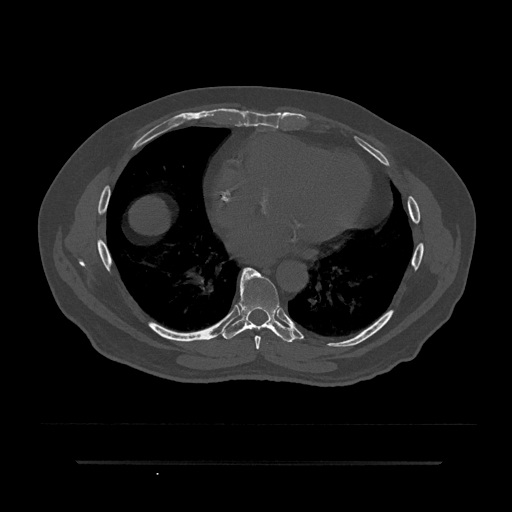
CT including the spine, one axial slice; slice 444 of 797 in the series (ordered by position); bone window (W 1800 / L 400 HU); 0.5 mm slice thickness; 512 × 512 image matrix. Patient: male, 59 years. Case-level facts recorded for this patient, not image findings: primary cancer: bile ducts; vertebrae with lytic lesions (as recorded): T10.
Structures marked on this image (semi-automatically segmented with operator editing):
- T7 vertebra: bounding box [x1, y1, x2, y2] px = [241, 268, 261, 349]
- T8 vertebra: [221, 268, 295, 343]